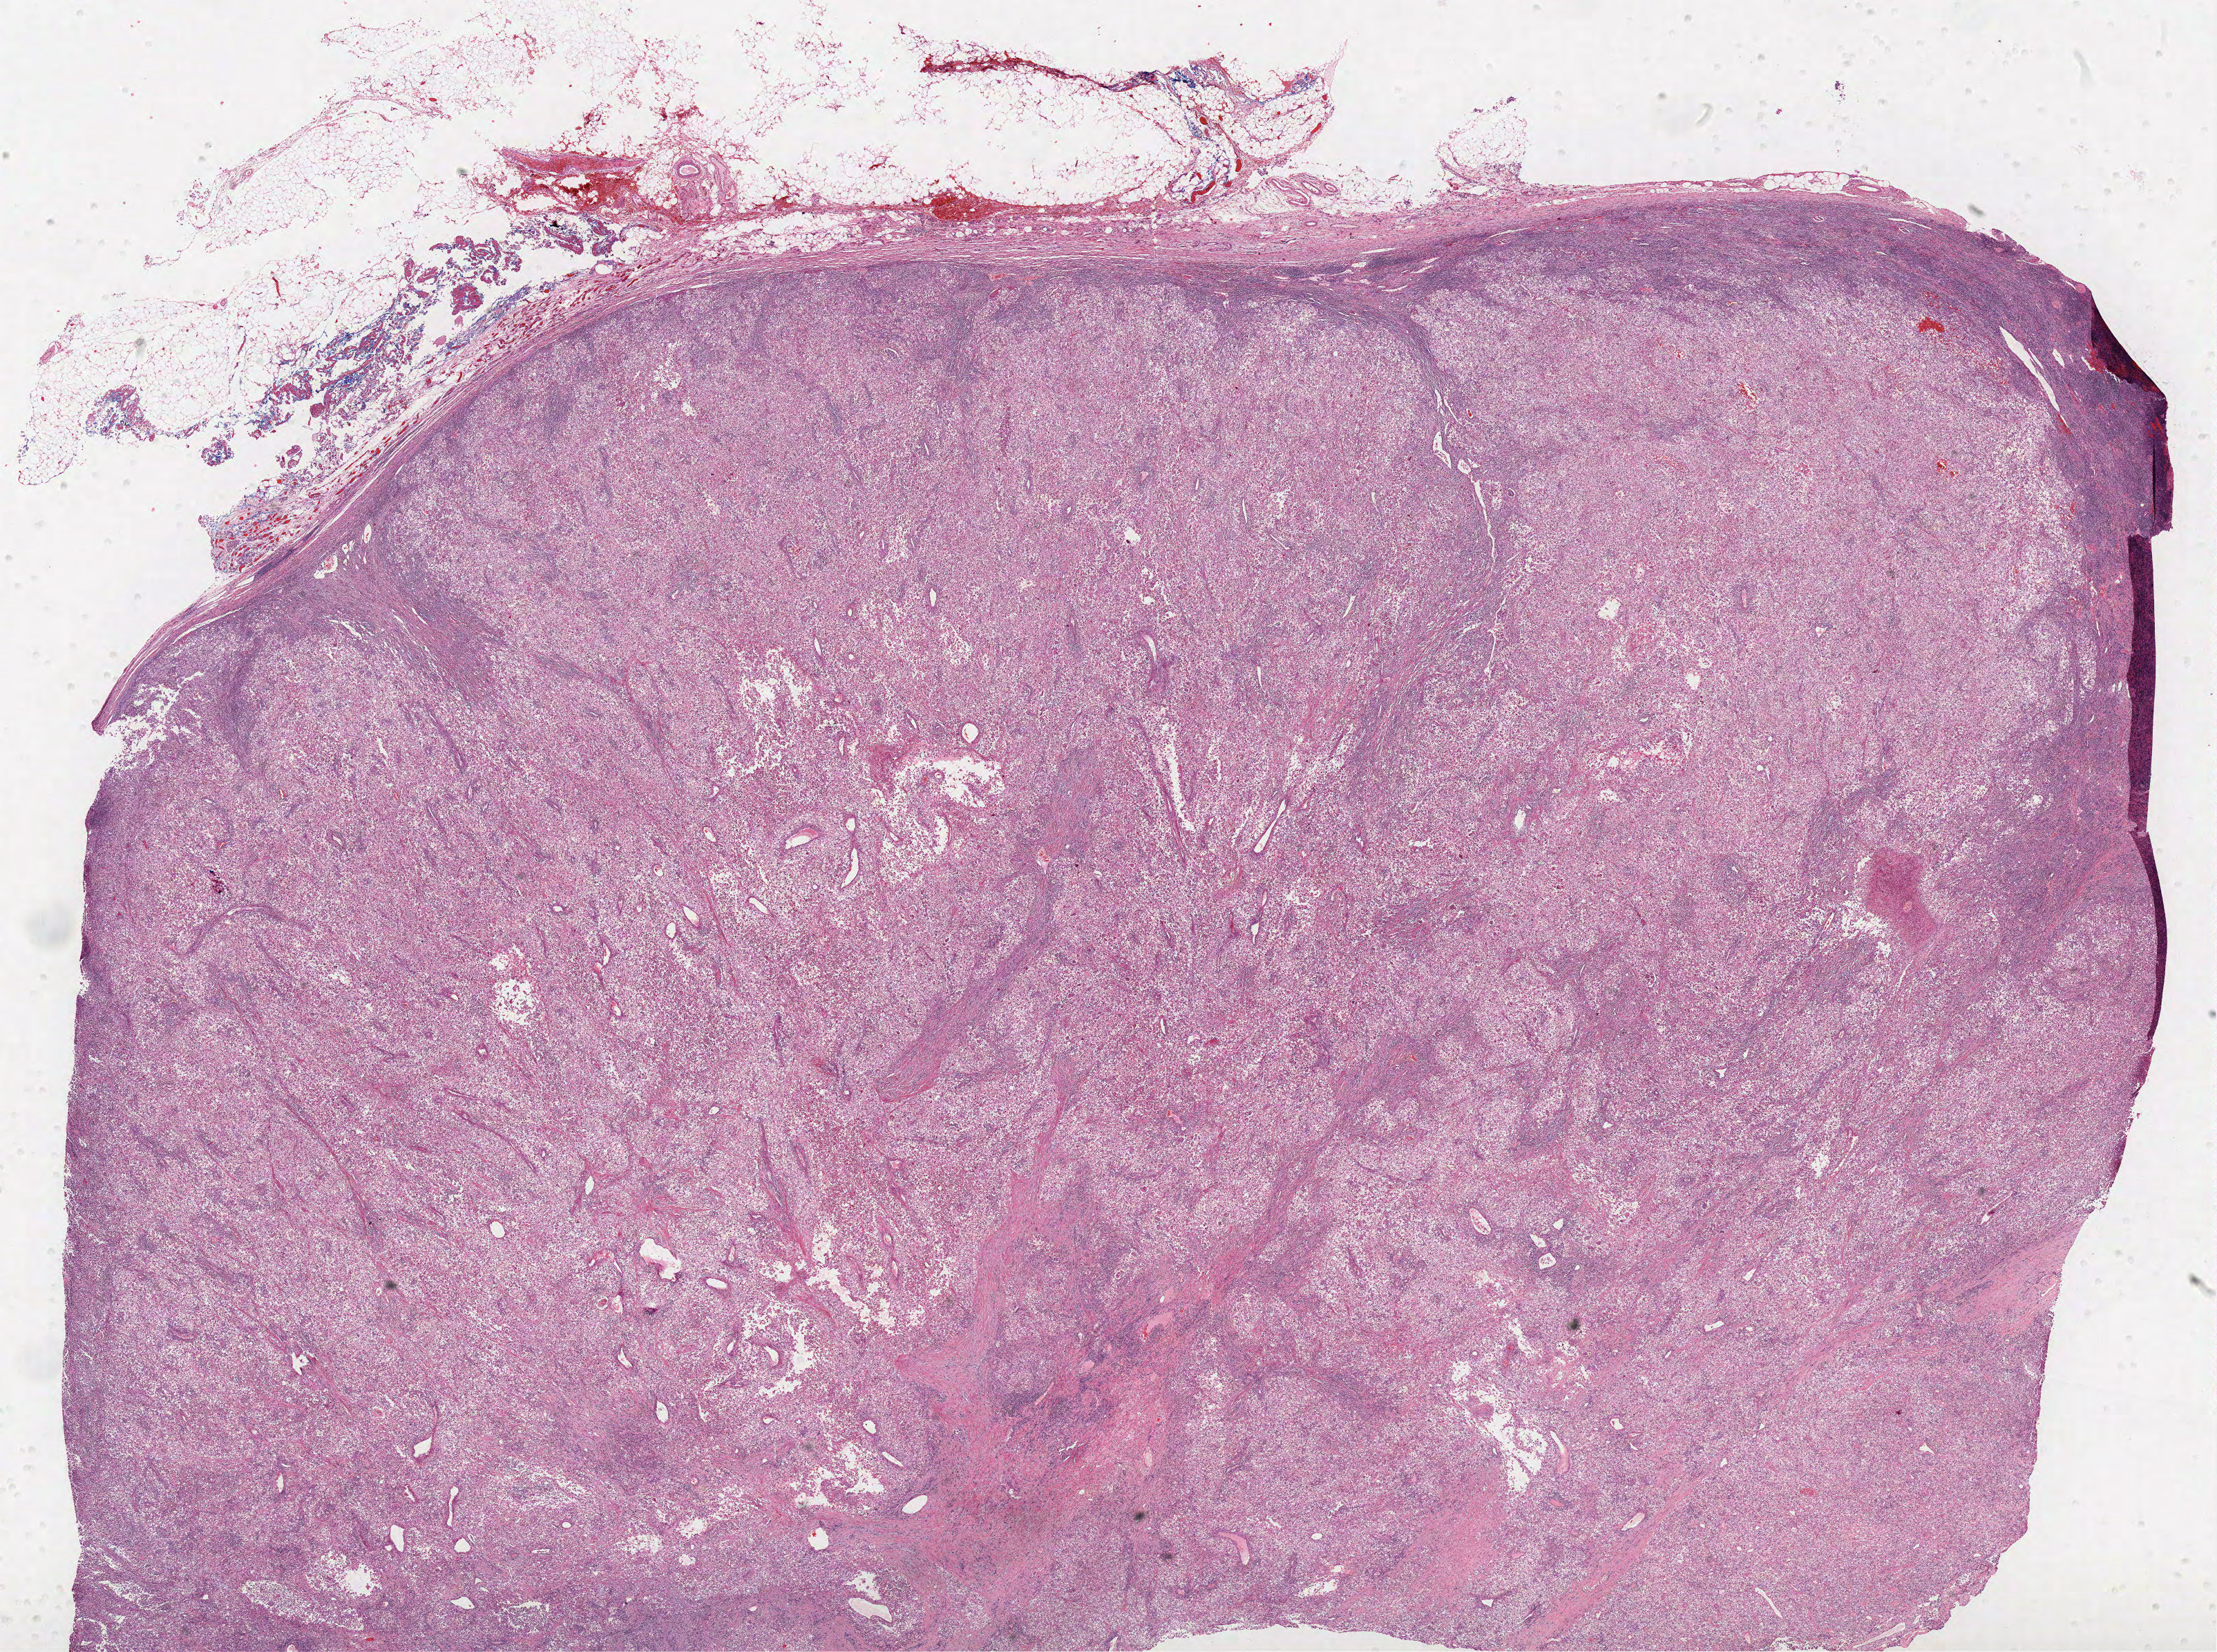
Hematoxylin and eosin (H&E) stained whole-slide image — whole scanned area (about 25.7 x 19.1 mm, from a 40x scan) shown as a low-resolution overview. Formalin-fixed paraffin-embedded (FFPE) diagnostic section. Kidney, primary tumour sample. Patient: female, age at initial diagnosis 67 years. Histologic grade: G4 (undifferentiated).
AJCC pathologic stage: III. Diagnosis: Clear cell adenocarcinoma, NOS.